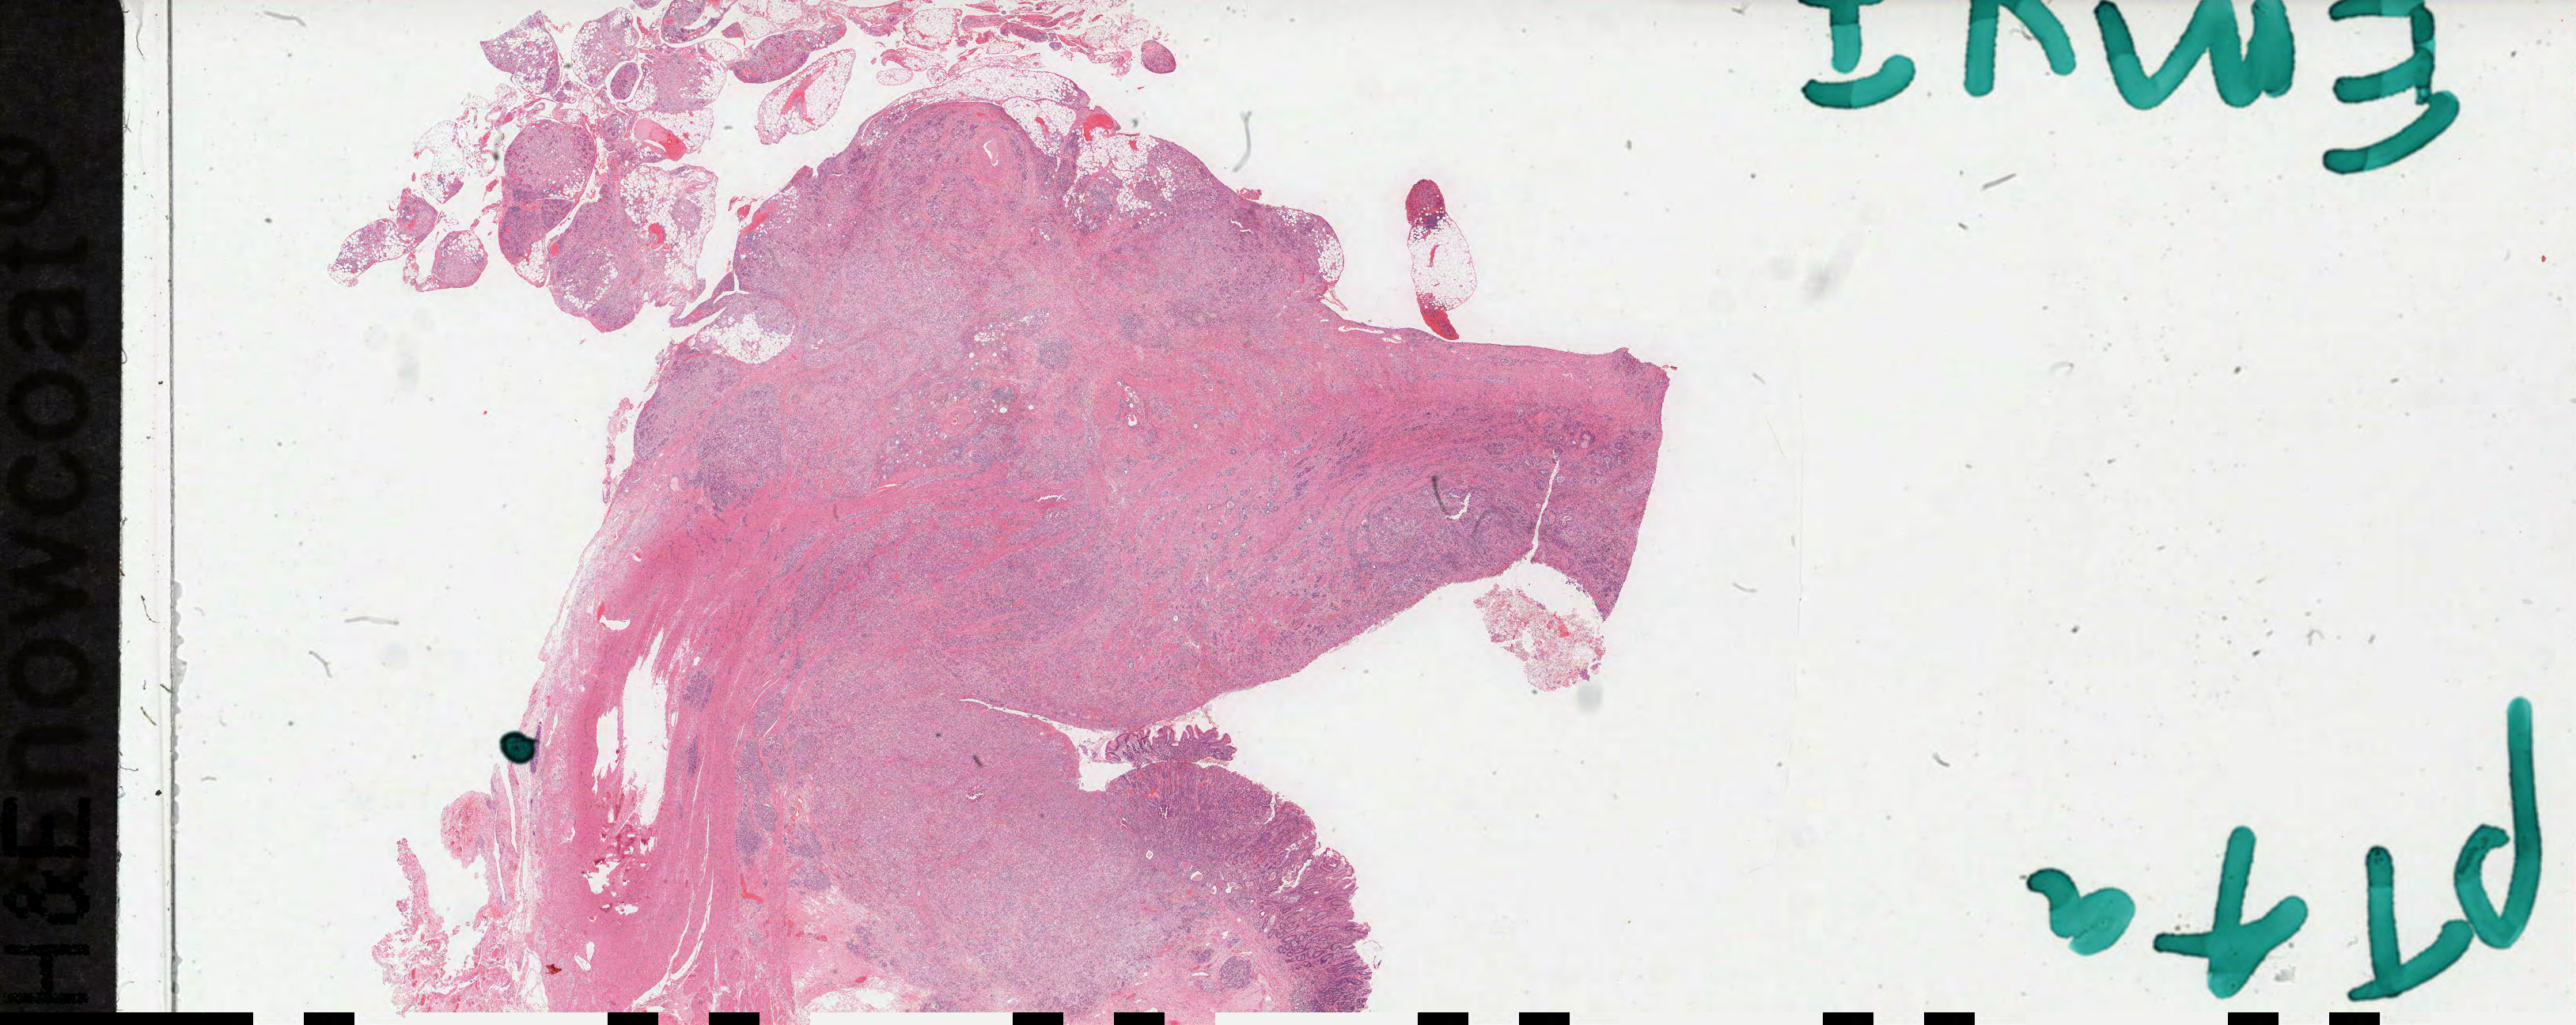
H&E whole-slide image — whole scanned area (about 52.7 x 21.0 mm) shown as a low-resolution overview; formalin-fixed paraffin-embedded (FFPE) diagnostic section; stomach, primary tumour sample. Patient: female, age at initial diagnosis 79 years. Histologic grade: G3 (poorly differentiated).
* lymph nodes positive (case pathology): 9 of 13 examined
* diagnosis: Tubular adenocarcinoma (gastric antrum)
* AJCC pathologic stage: IIIC (7th edition)